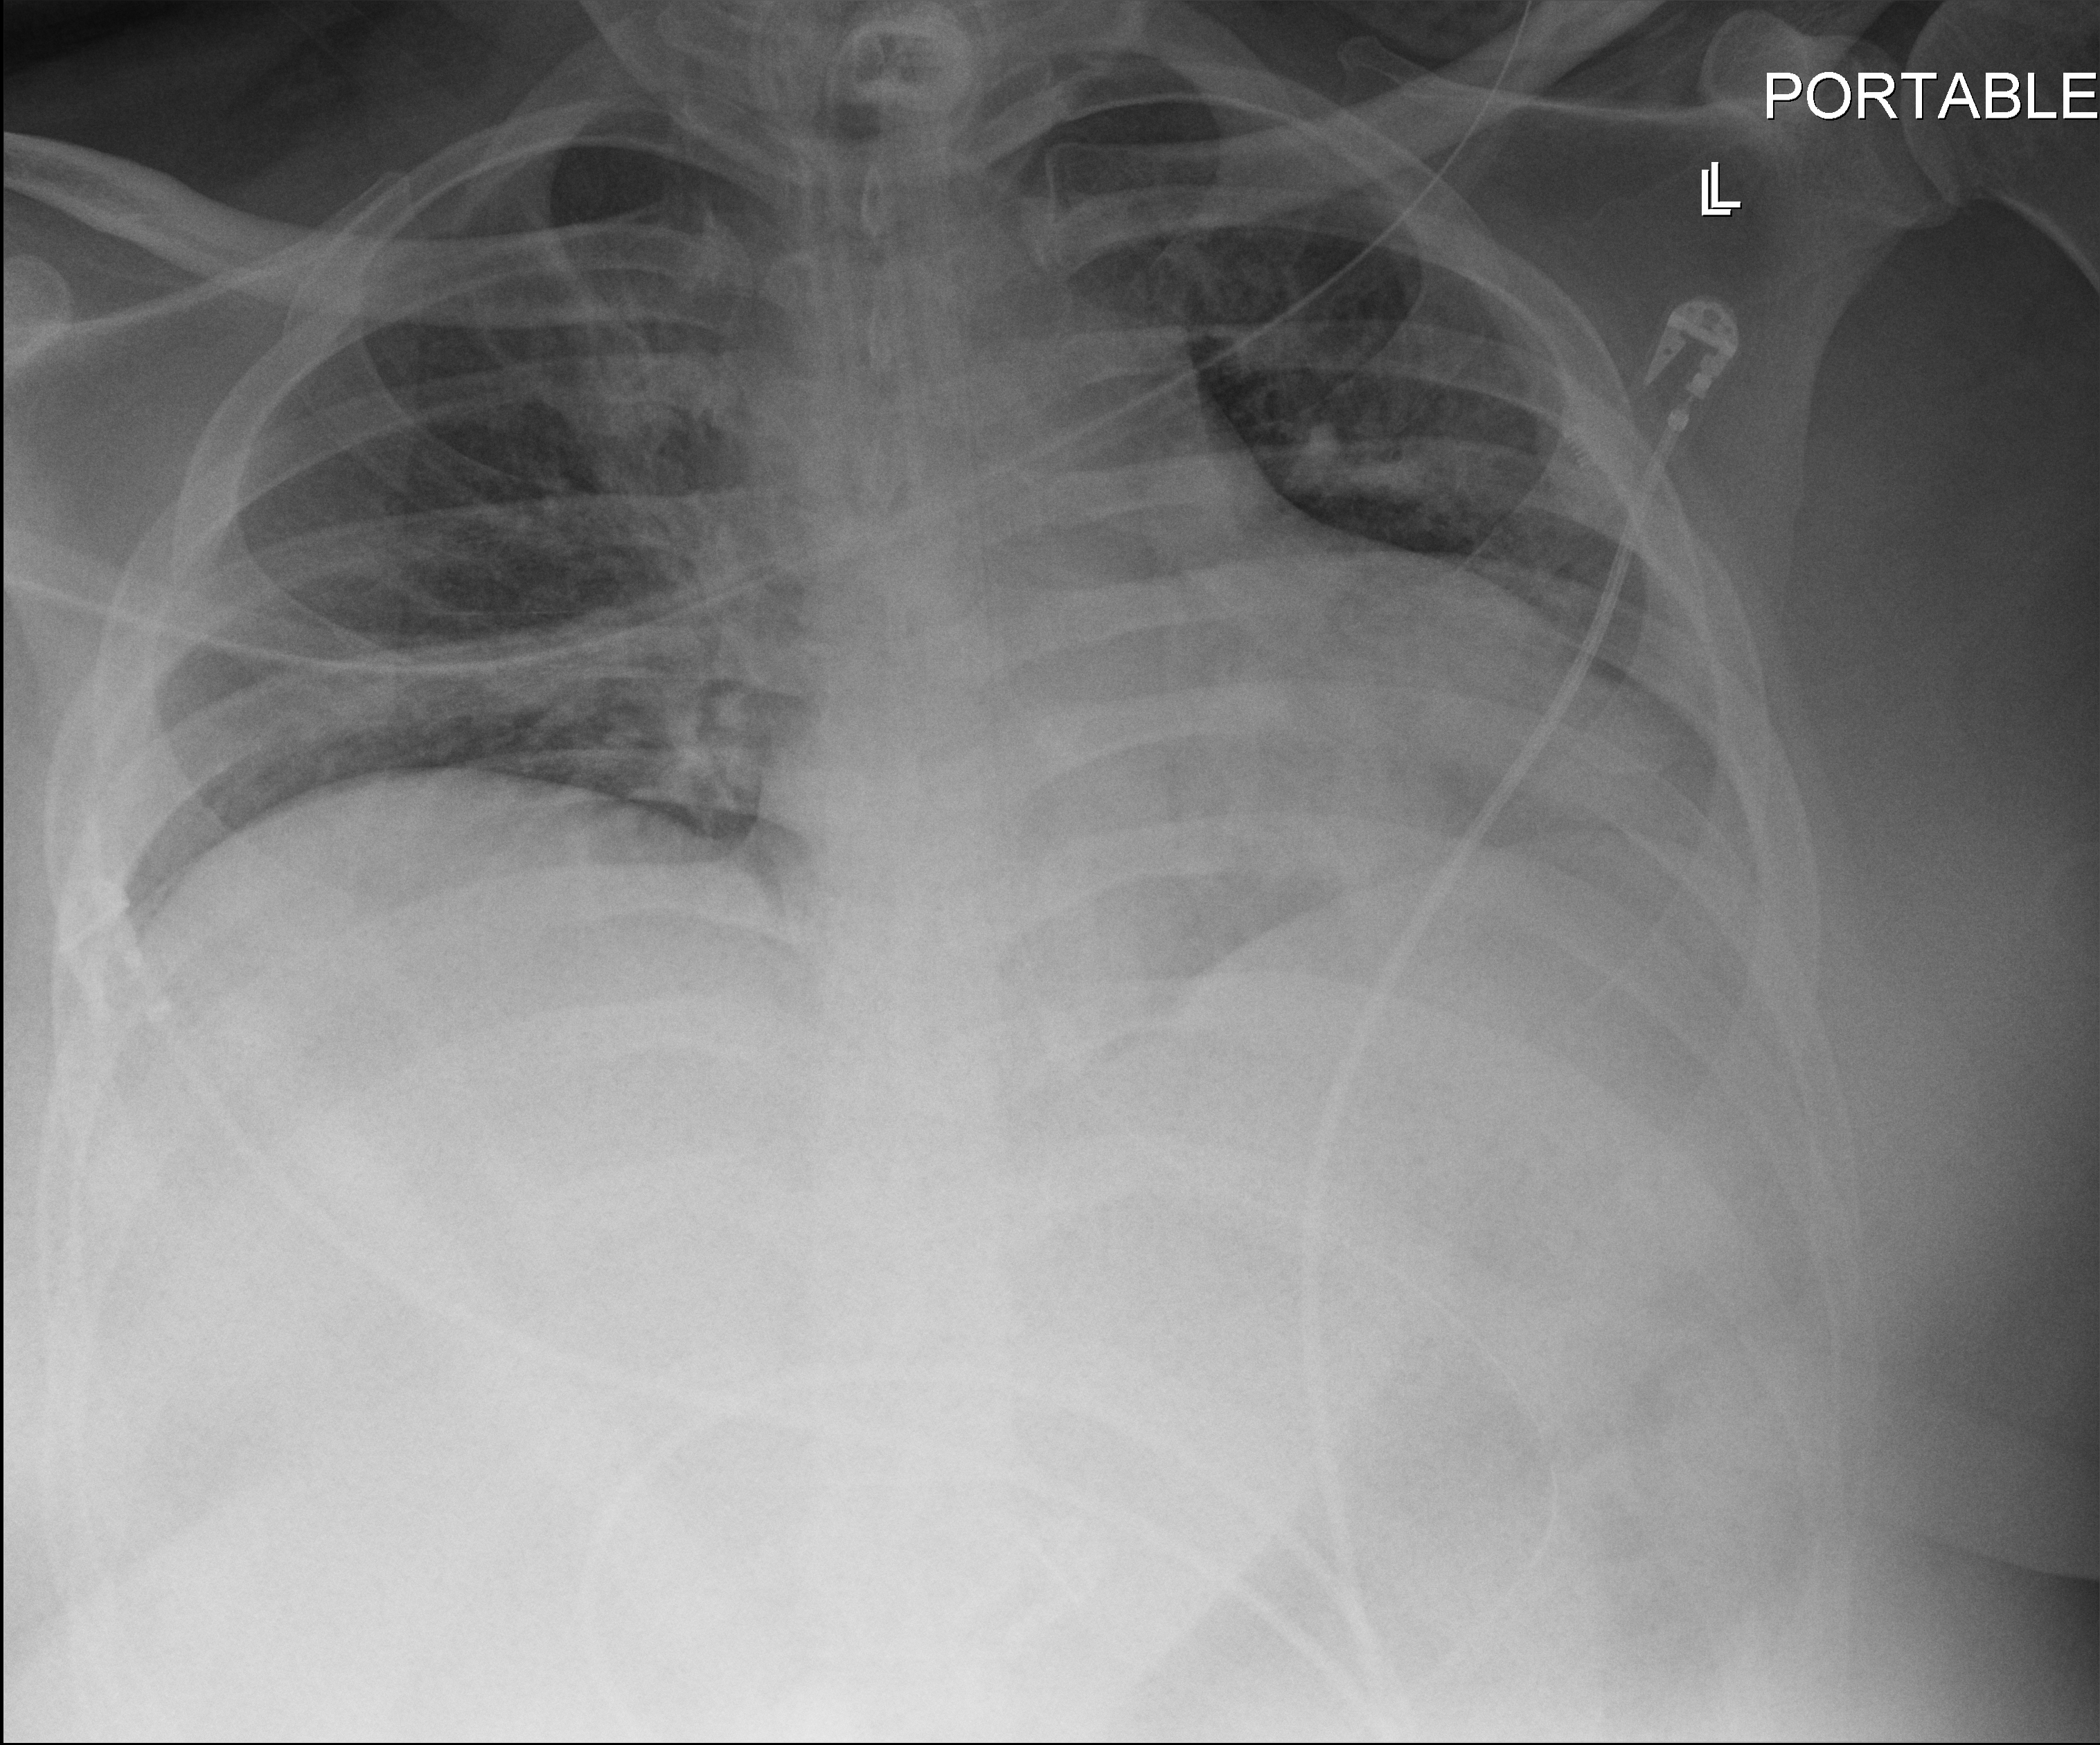
Chest X-ray (portable), anteroposterior (AP) projection. Male patient hospitalised with COVID-19, age 18–59 years.
Hospital-stay facts (about this admission, not read from this image; timing relative to this image not recorded):
- mechanically ventilated during this hospital stay: yes
- other chronic lung disease (admission record): yes
- length of hospital stay: 69 days